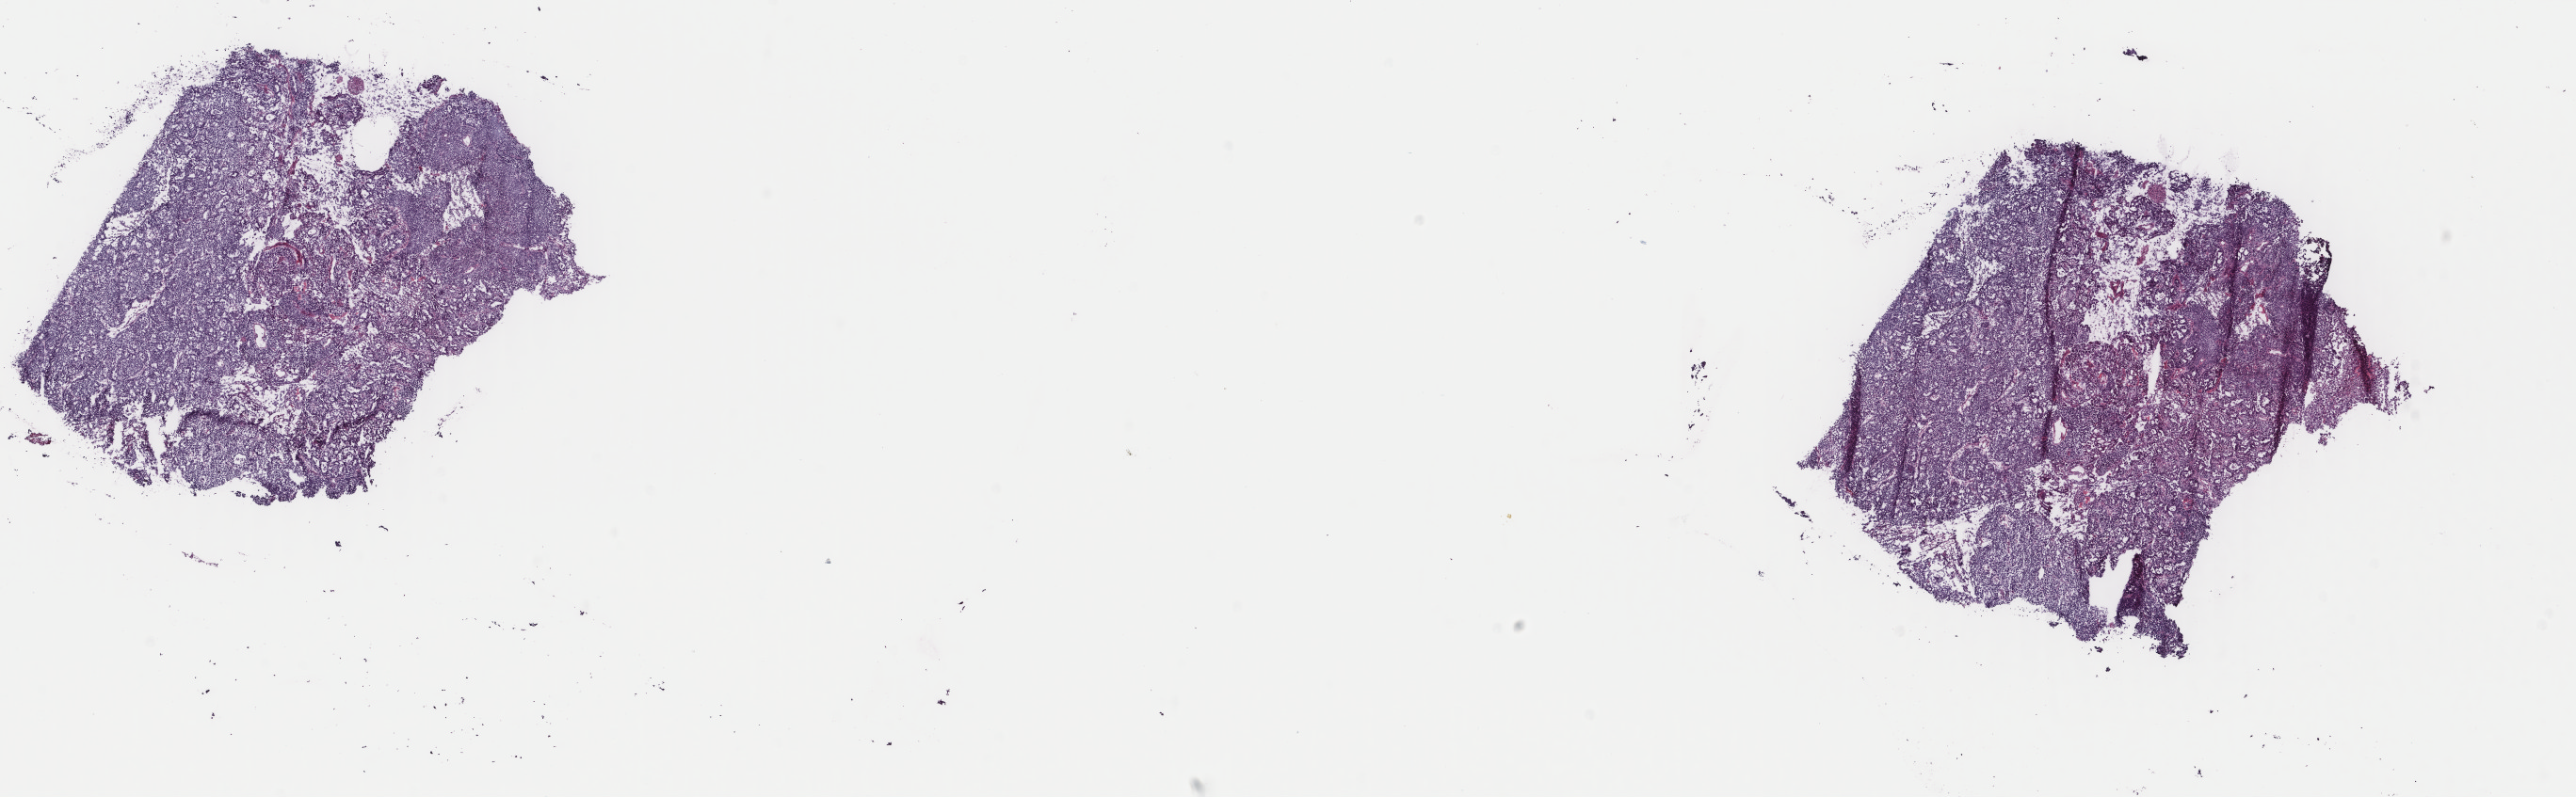
Digitized H&E-stained tissue section (whole slide) — whole scanned area (about 21.7 x 6.7 mm) shown as a low-resolution overview; frozen section from the top of the tissue portion; sample: primary tumour, uterus. Female, age 53 years at initial diagnosis. Histologic grade: G3 (poorly differentiated). Slide review estimates, as recorded: tumour cells 90%, tumour nuclei 90%, normal cells 0%, stromal cells 5%, necrosis 5%. Inflammatory infiltration, as recorded: lymphocyte infiltration 40%, monocyte infiltration 20%, neutrophil infiltration 20%.
- diagnosis: Serous cystadenocarcinoma, NOS (endometrium)
- FIGO stage: IVB